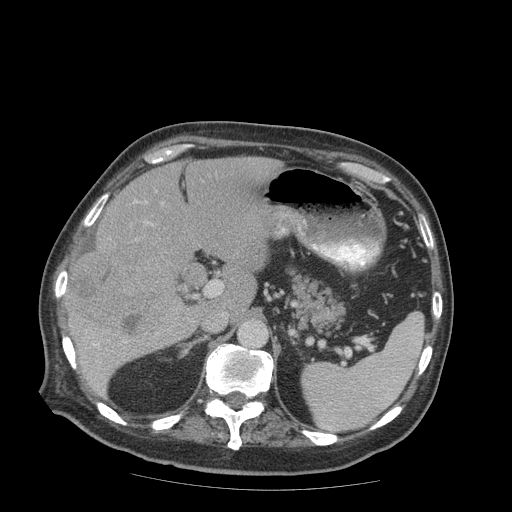
Contrast-enhanced abdominal CT (liver protocol), one axial slice. Slice 51 of 99 in the series (ordered by position). Reconstruction kernel STANDARD. Soft-tissue window (W 400 / L 40 HU). 2.5 mm slice thickness. 512 × 512 image matrix. Case-level facts recorded for this patient, not image findings: diagnosis: hepatocellular carcinoma (patient treated with transarterial chemoembolisation; whether this scan precedes or follows treatment is not stated here); TNM stage (as recorded): Stage-IIIB; Child-Pugh class: A; tumour nodularity: multinodular.
Outlined on this slice (semi-automatic segmentation, software-assisted and operator-edited):
- liver parenchyma outside the tumour (the mass and vessels are separate outlines, so this box may not span the whole liver): box from (x=68, y=156) to (x=282, y=396) px
- mass: (x=62, y=252)–(x=174, y=343)
- liver vessels: (x=94, y=200)–(x=137, y=346)